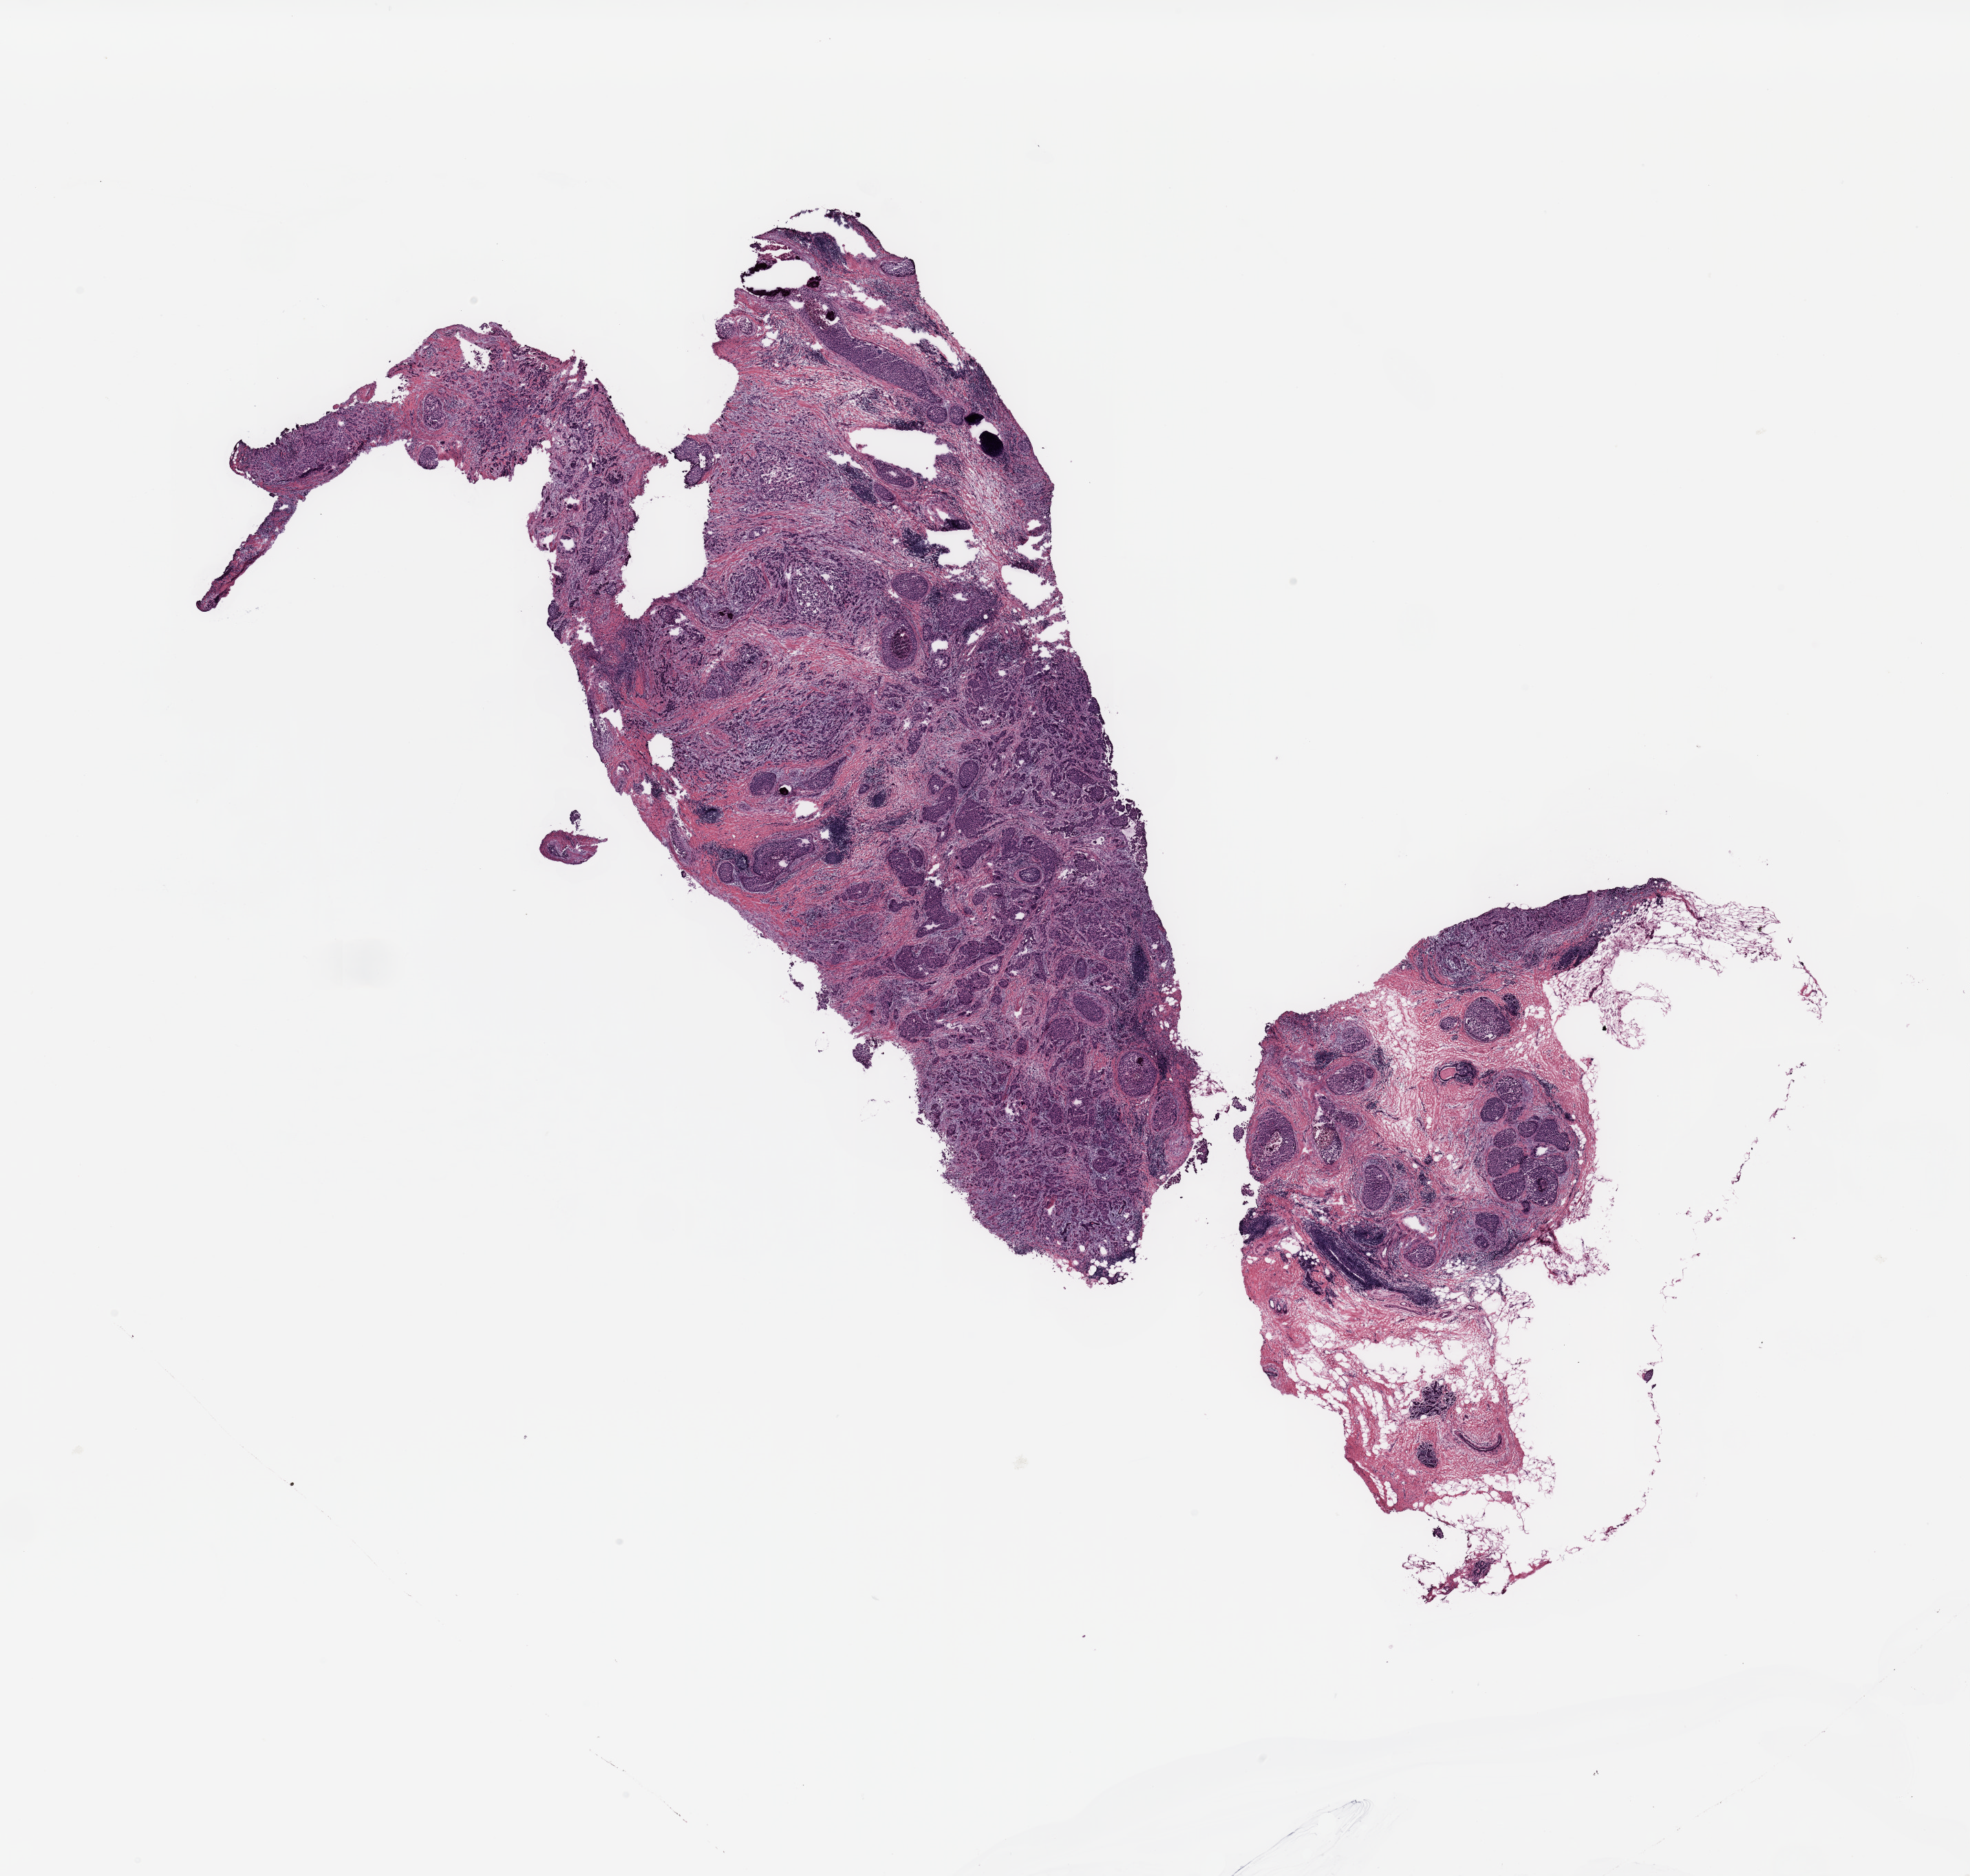
Whole-slide histology image, H&E-stained, low-resolution overview of the scanned area, about 22.6 x 21.6 mm (slide scanned at 20x); breast, tissue type not recorded.
Patient diagnosis (cohort enrolment): breast cancer (breast).